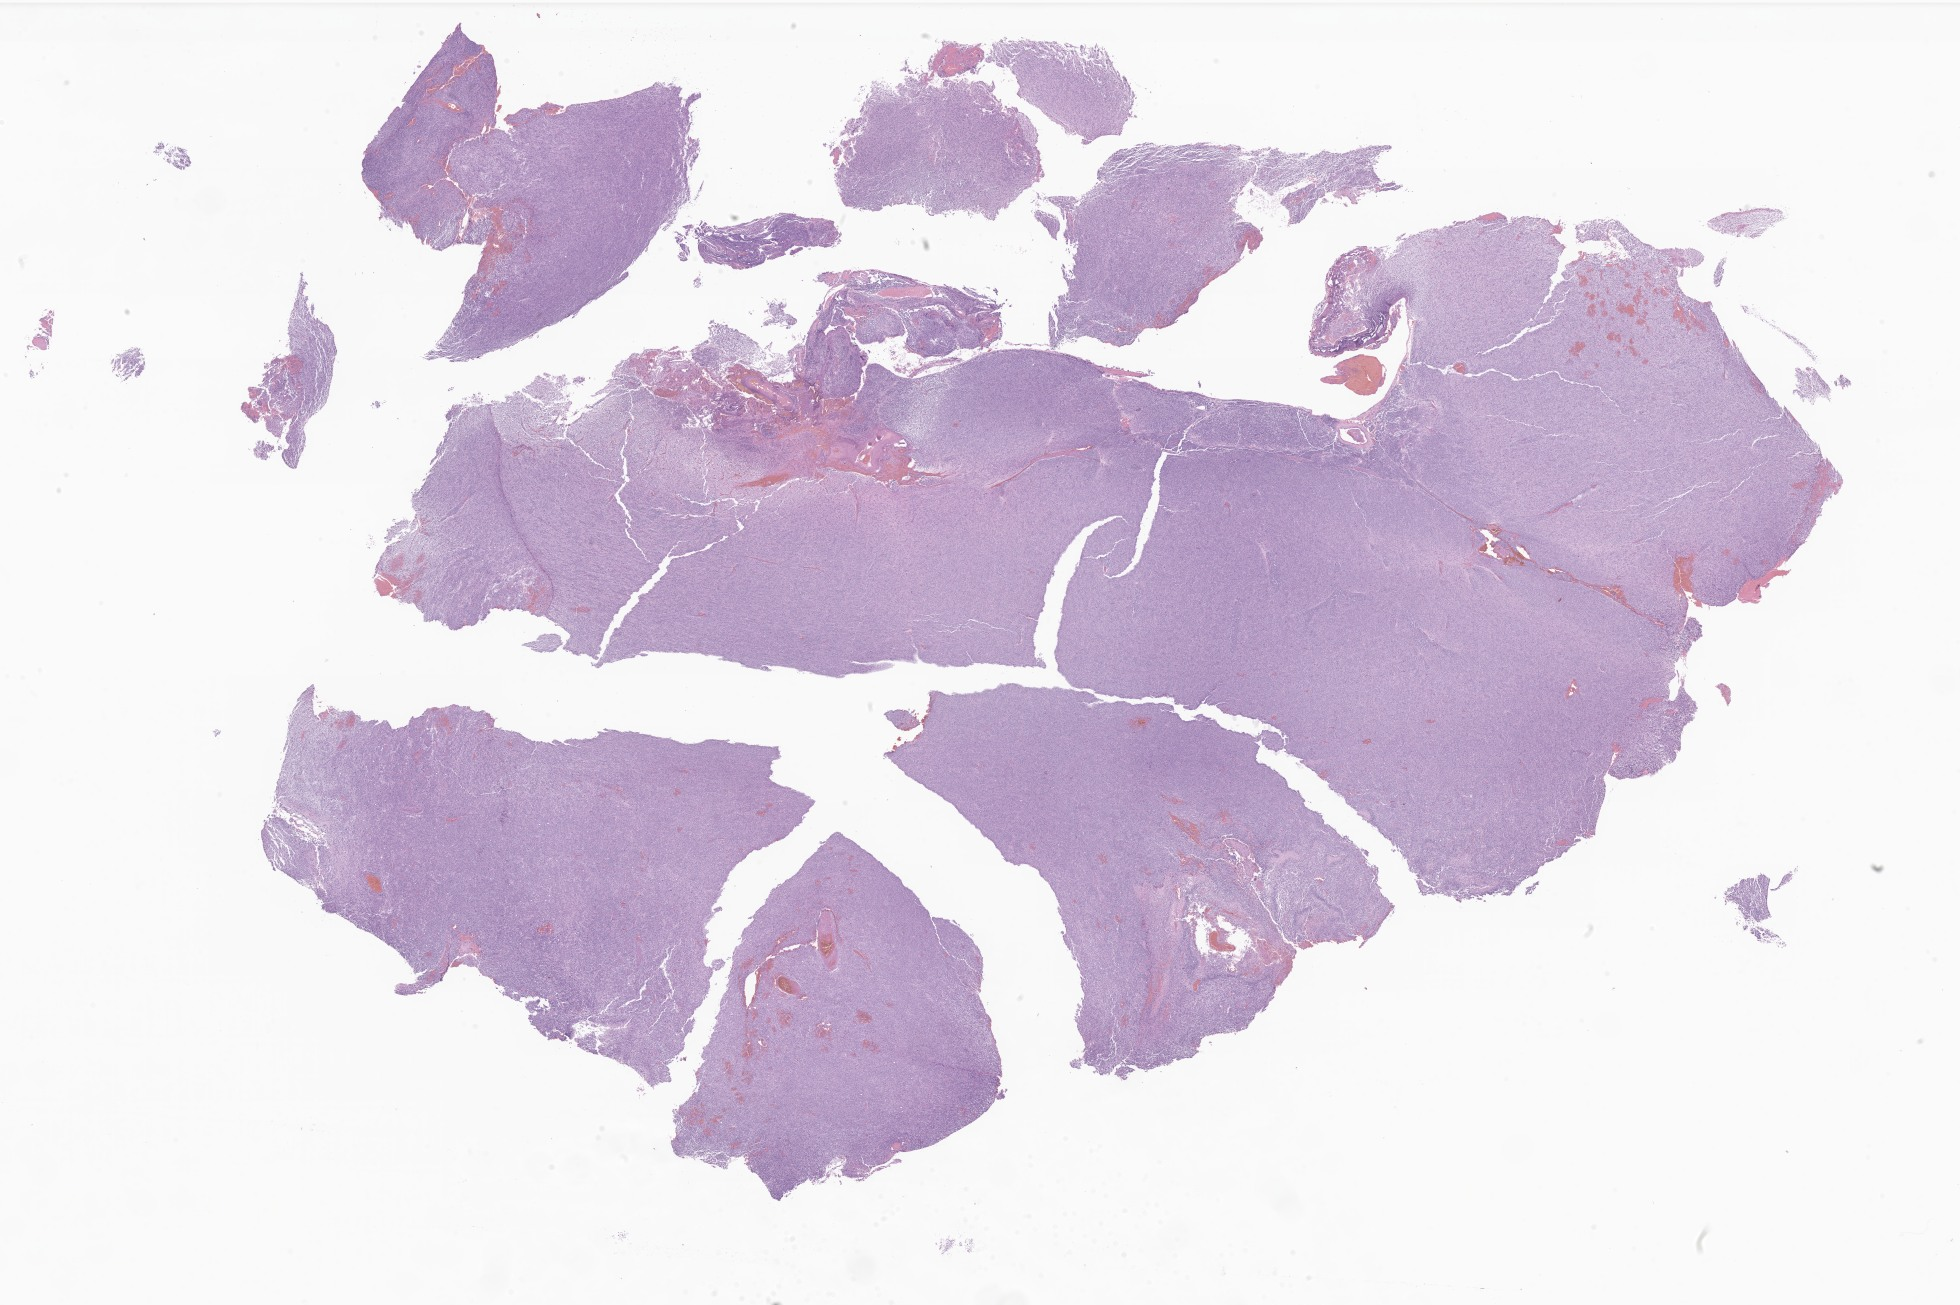
Digitized haematoxylin and eosin-stained section of tumor tissue from the brain, shown as a low-resolution overview of the whole scanned area (about 33.1 x 22.0 mm). Formalin-fixed, paraffin-embedded (FFPE) tissue. Patient: female, age 142 months.
Diagnosis: Glioma, malignant.